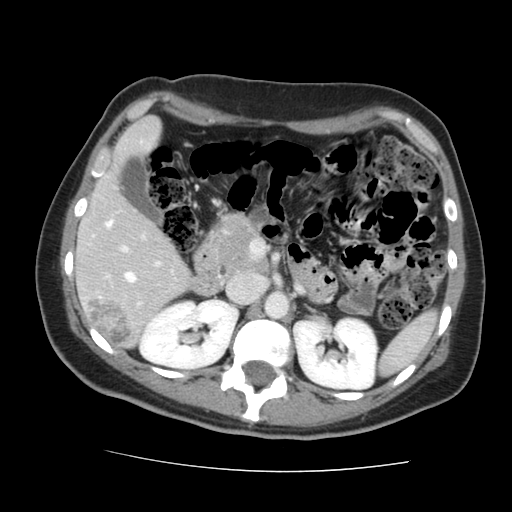
Contrast-enhanced abdominal CT, one axial slice. Slice 80 of 144 in the series (ordered by position). 120 kVp. Intravenous contrast given. Soft-tissue window (W 400 / L 40 HU). 2.5 mm slice thickness. 512 × 512 image matrix. Female patient, age 46 years. Case-level facts recorded for this patient, not image findings: diagnosis: colorectal cancer liver metastases, imaged before liver resection.
Outlined on this slice (expert manual segmentation):
- hepatic veins: bounding box (x1, y1, x2, y2) in pixels: (125, 272, 136, 282)
- liver: (78, 119, 191, 347)
- planned liver remnant (the part of the liver to remain after resection): (78, 119, 191, 344)
- portal vein (with intrahepatic branches): (105, 221, 161, 305)
- liver metastasis: (90, 298, 135, 345)